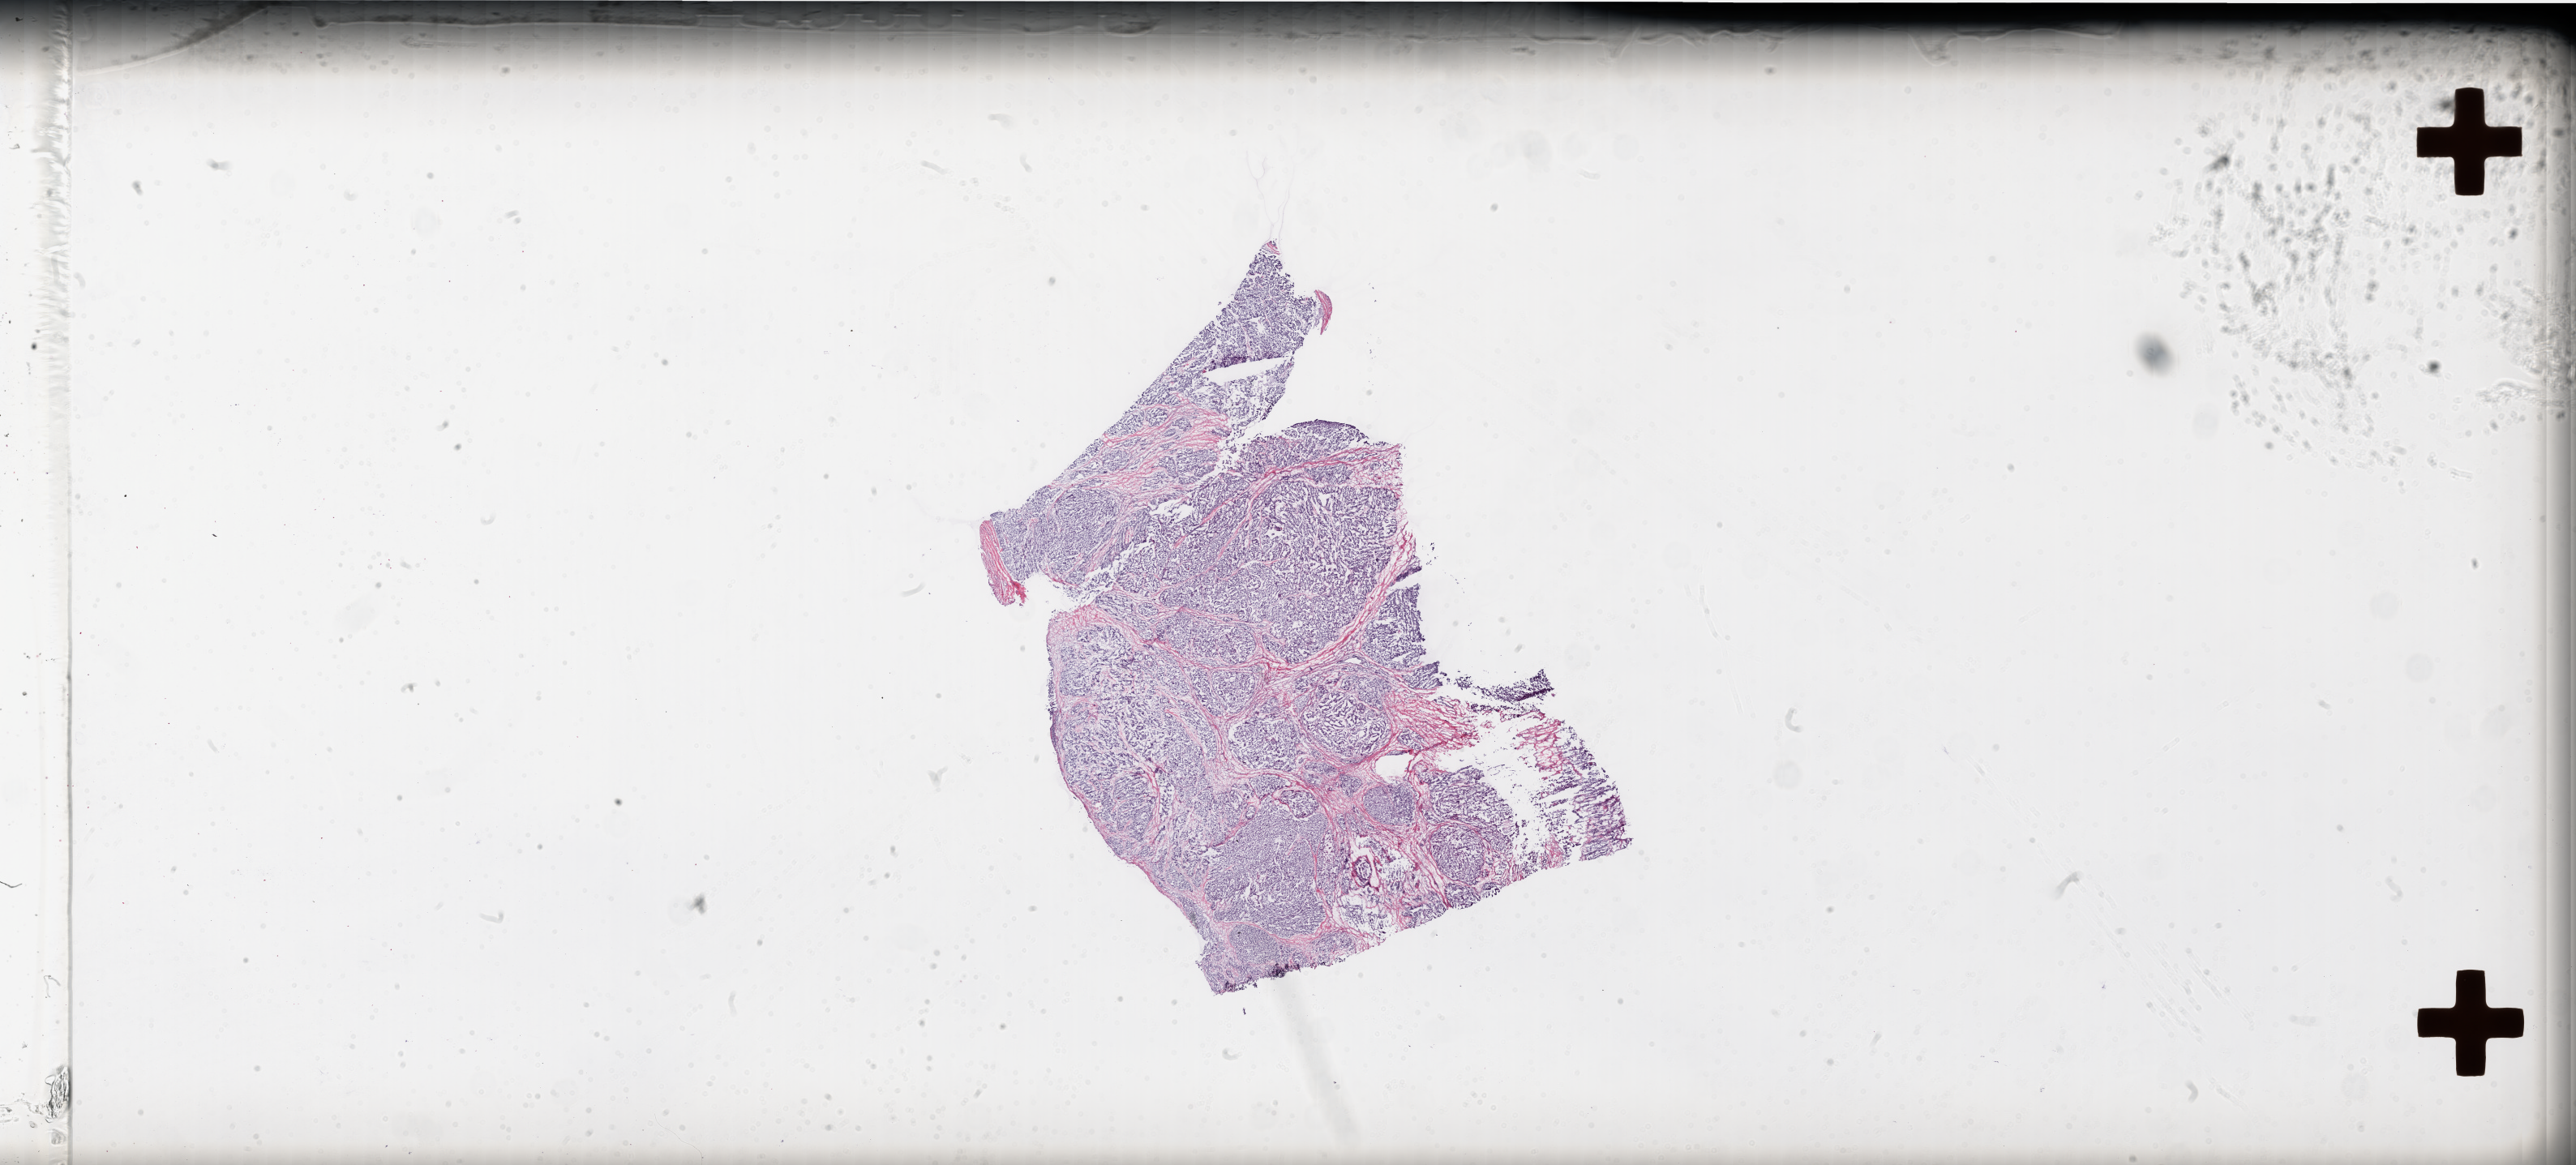
Whole-slide histology image, H&E-stained — low-resolution overview of the scanned area, about 51.1 x 23.1 mm (from a 20x scan), frozen section from the top of the tissue portion, ovary, primary tumour sample. Patient: female, age at initial diagnosis 81 years. Histologic grade: G3 (poorly differentiated). Pathologist review of this section (percent, as recorded): tumour cells 75%, tumour nuclei 90%, normal cells 0%, stromal cells 25%, necrosis 0%.
- pathologic diagnosis: Serous cystadenocarcinoma, NOS
- FIGO stage: IIIC